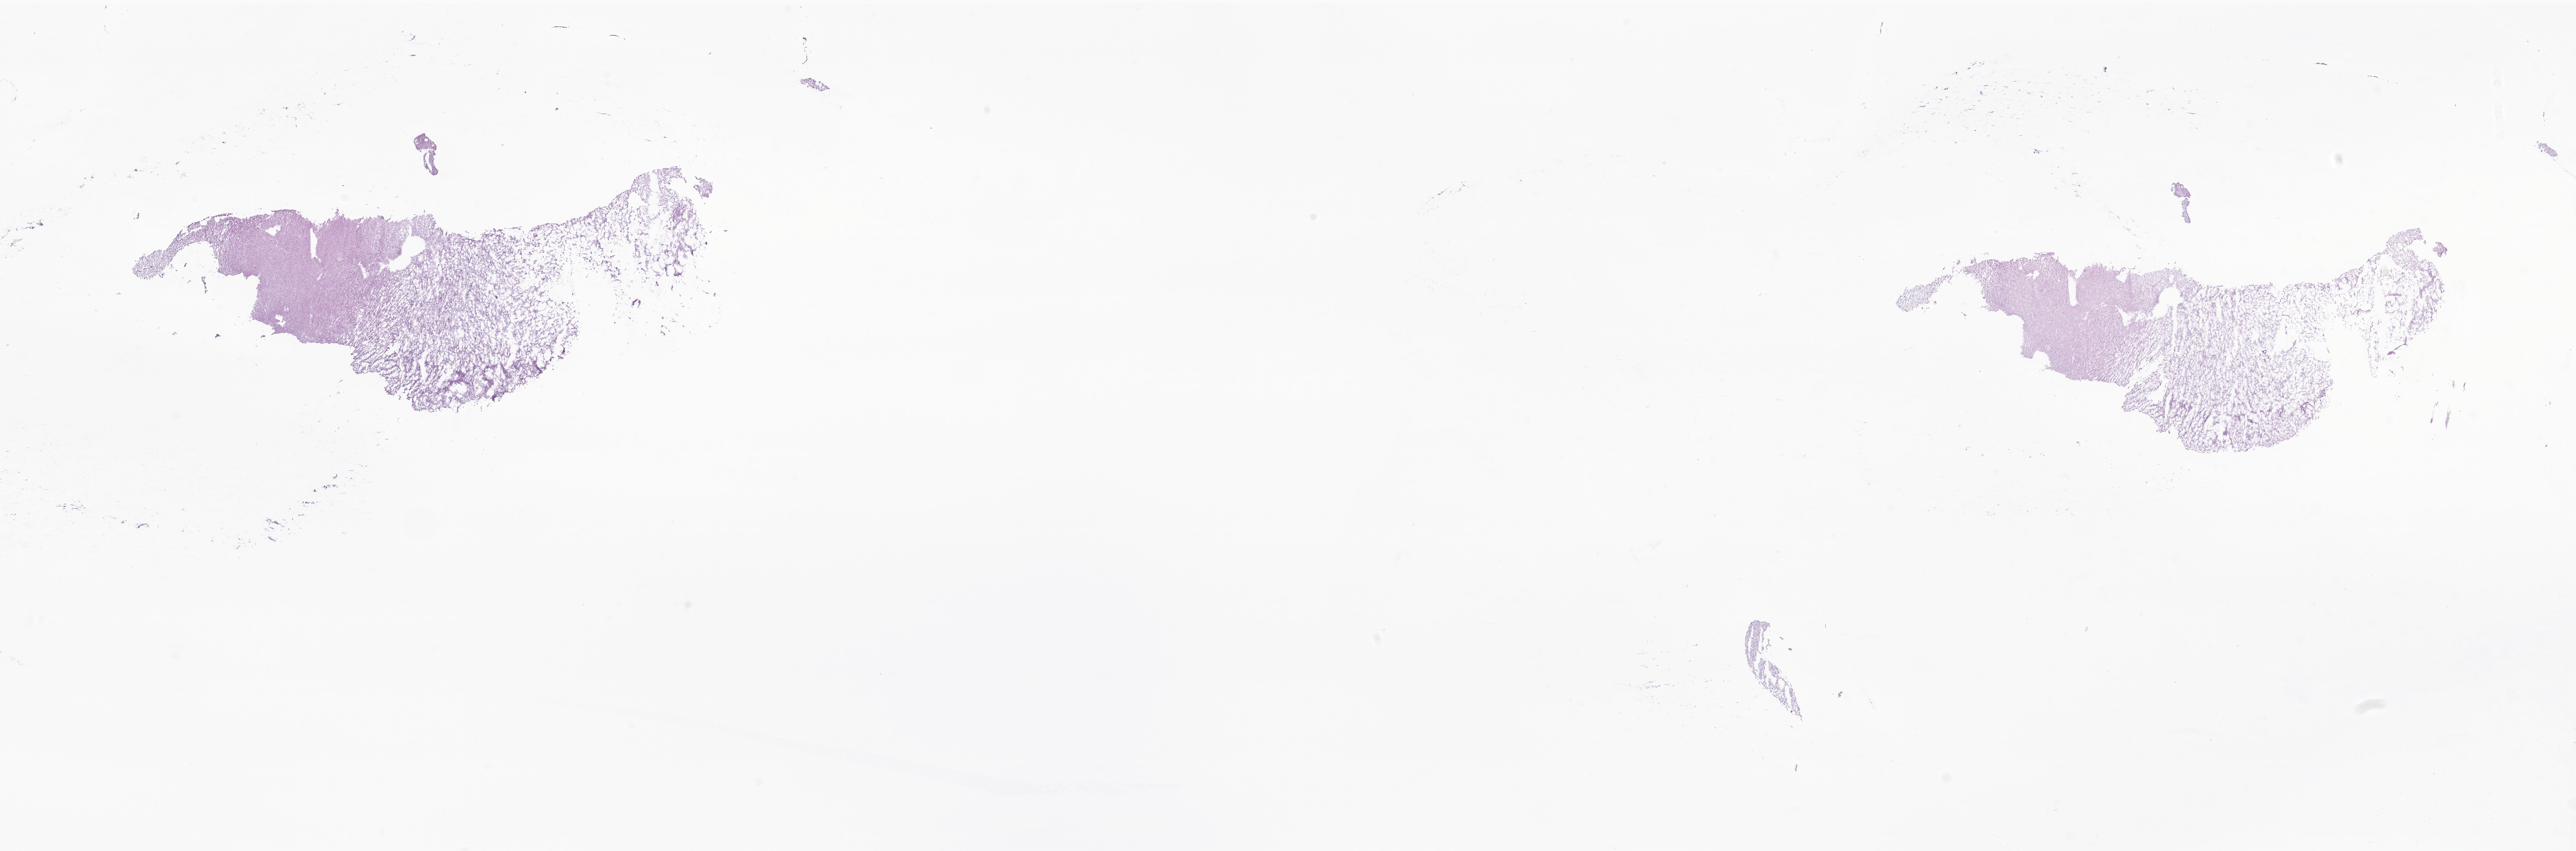
Whole-slide image, hematoxylin and eosin (H&E) stain of tumor tissue from the brain — whole scanned area (about 35.7 x 11.8 mm) shown as a low-resolution overview; cryosection (OCT / tissue freezing medium). Patient: male, age 167 months.
Recorded diagnosis: Neoplasm, uncertain whether benign or malignant.